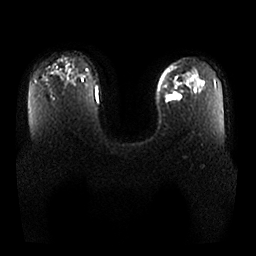
Breast MRI, one axial slice. Position 17 of 25 along the scan axis. Diffusion-weighted series; image 2 of 4 stored at this slice position (different b-values; order by instance number). 1.5 T. 256 × 256 image matrix, field of view 380 × 380 mm. Female patient.
Outlined on this slice (outlined manually by an expert reader):
- tumour on diffusion-weighted imaging: box from (x=165, y=92) to (x=181, y=101) px